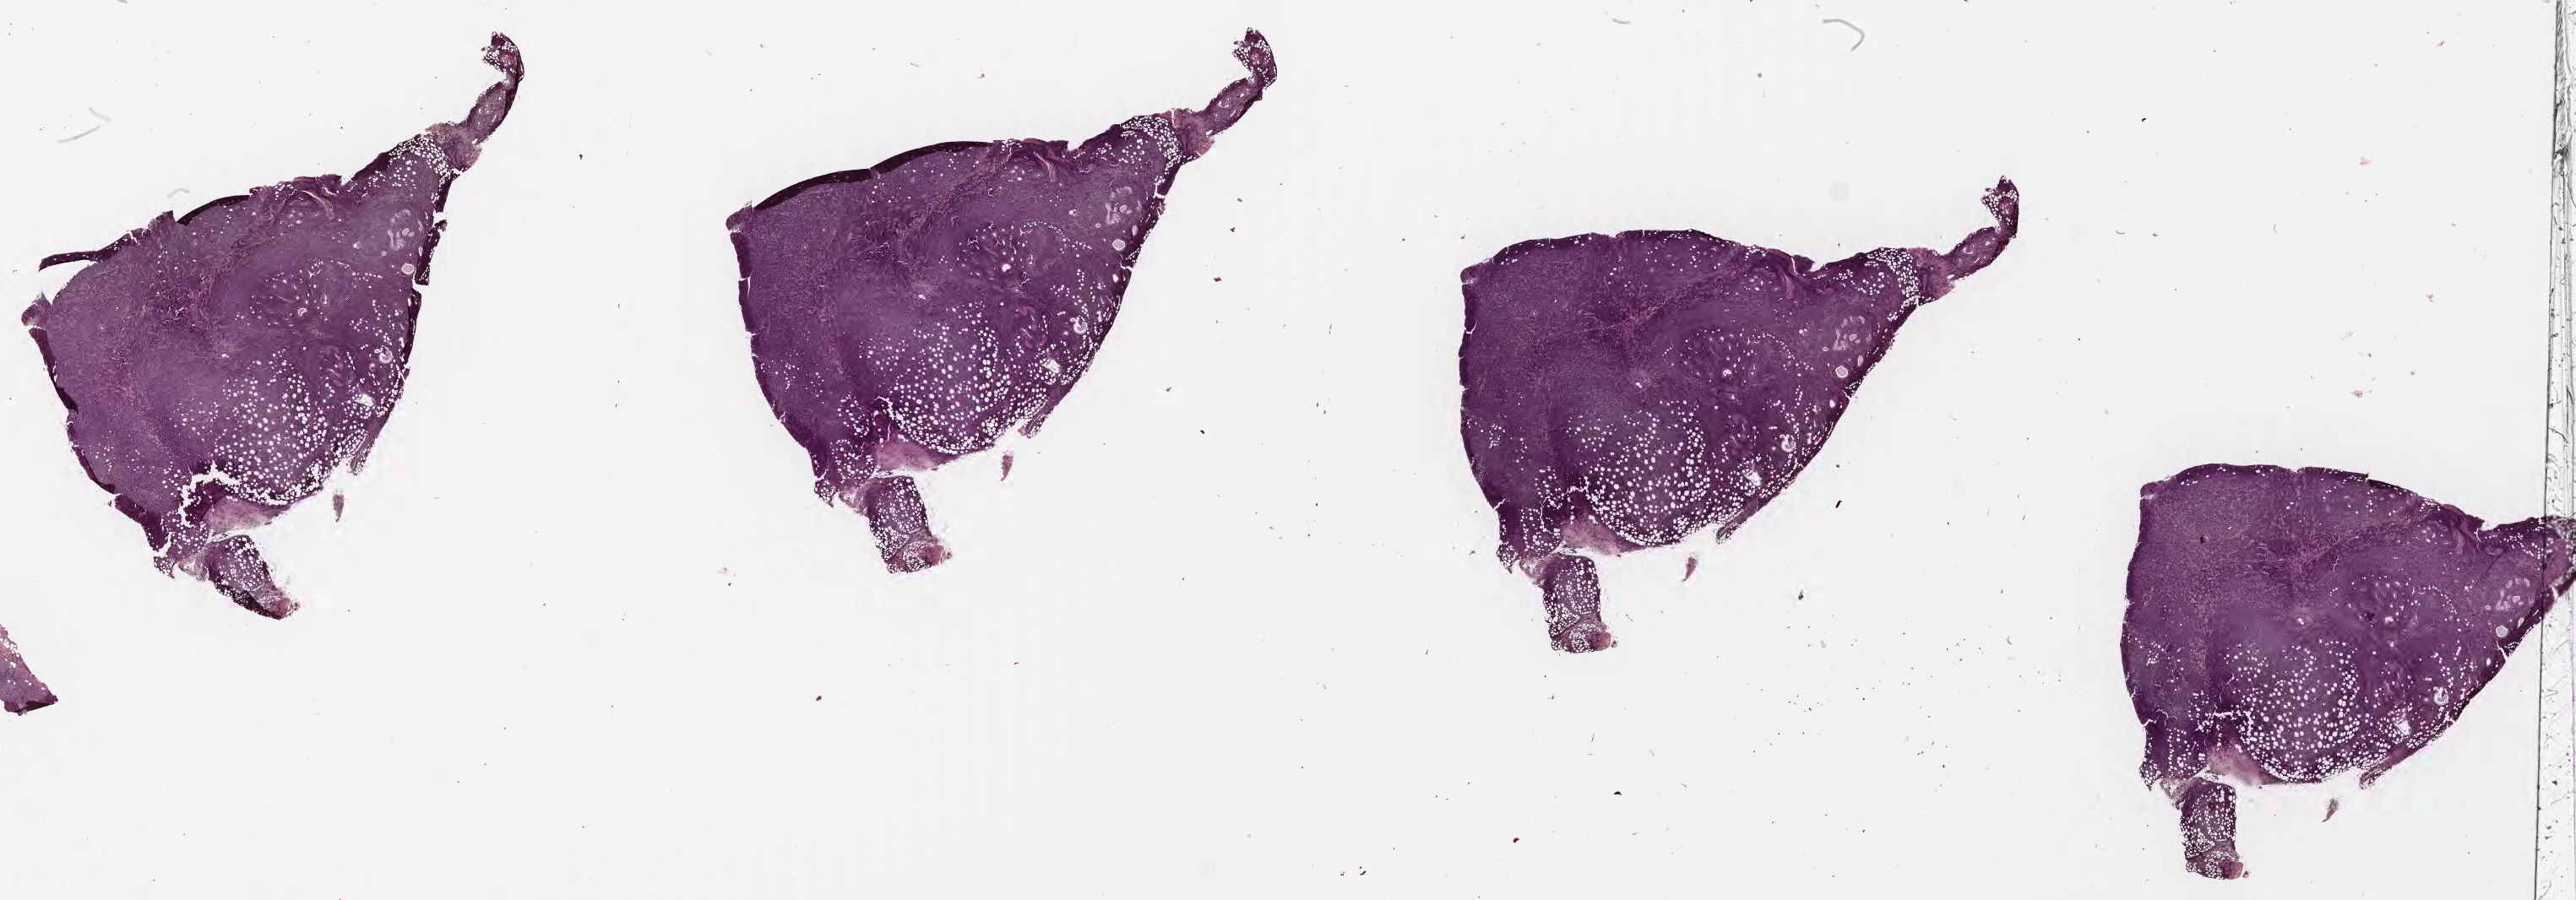
Digitized haematoxylin and eosin-stained section, a low-resolution overview of the entire scanned area, about 49.3 x 17.2 mm, tumor tissue. Patient: male, age 46 years.
Histologic diagnosis: Burkitt lymphoma, NOS.